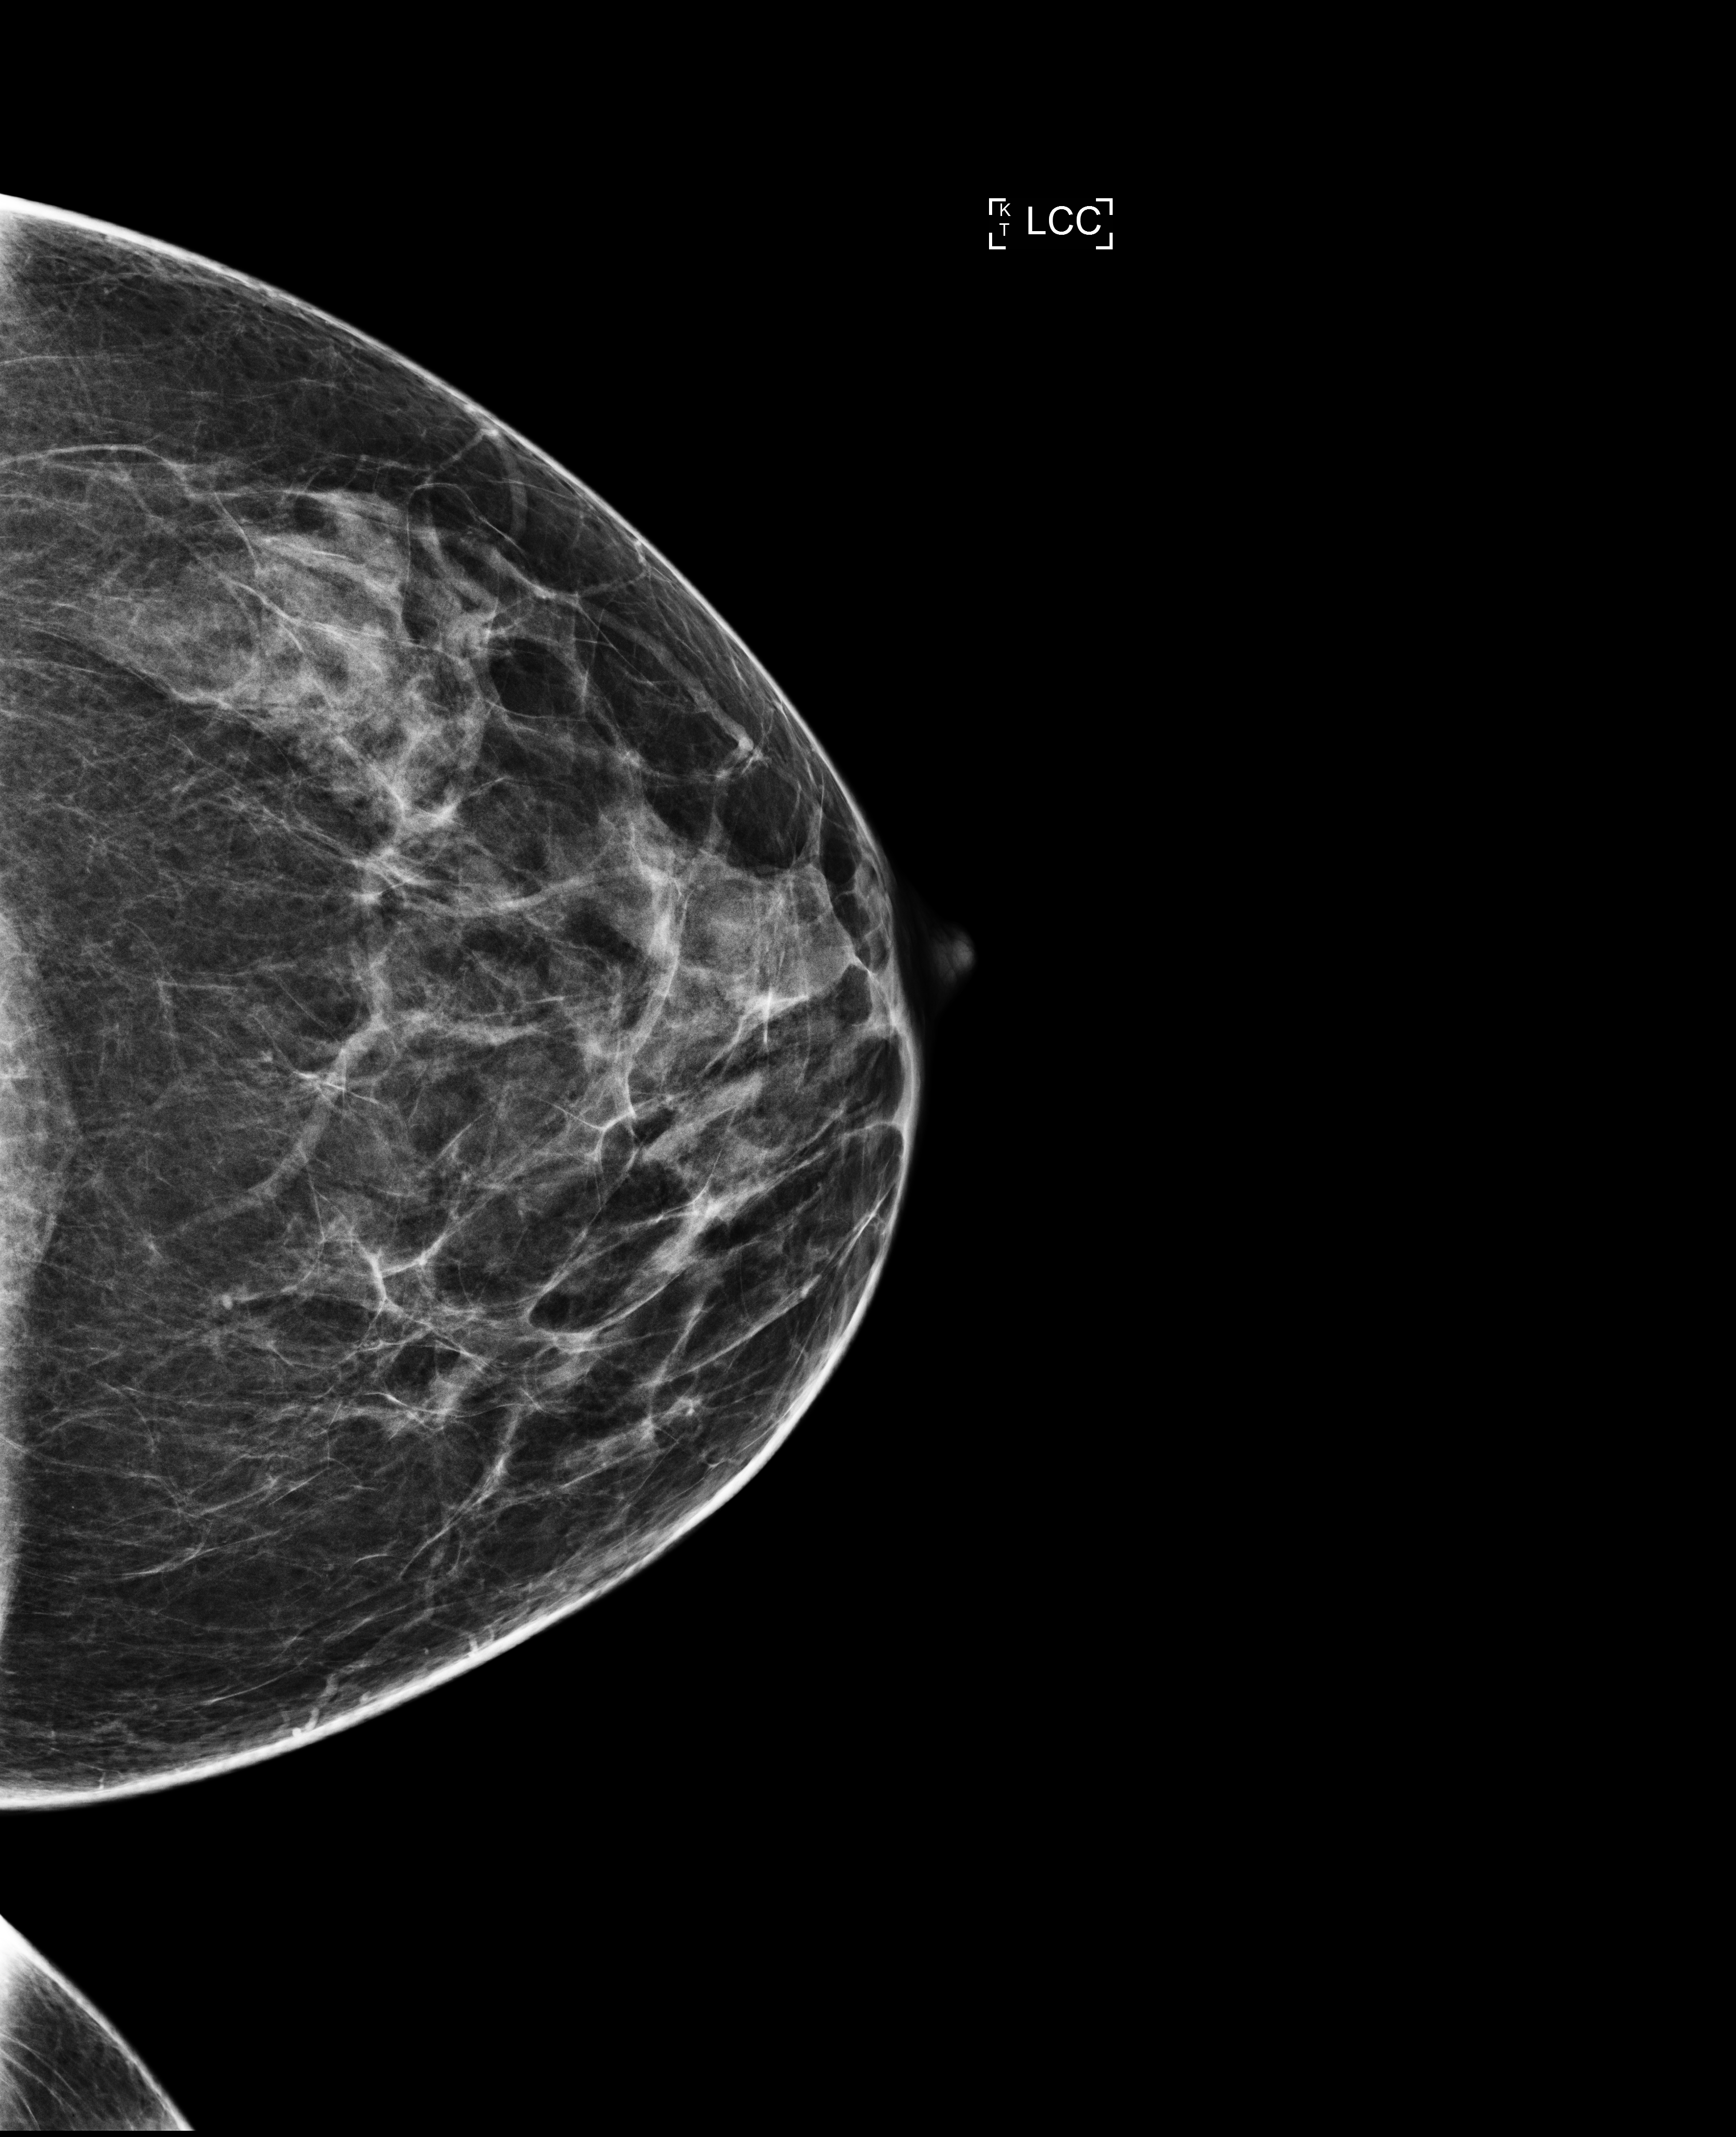
Annual screening mammography examination, compressed breast thickness 64 mm. Patient aged 54 years (female).
Image type: full-field digital mammogram. Breast: left. Projection: CC view.